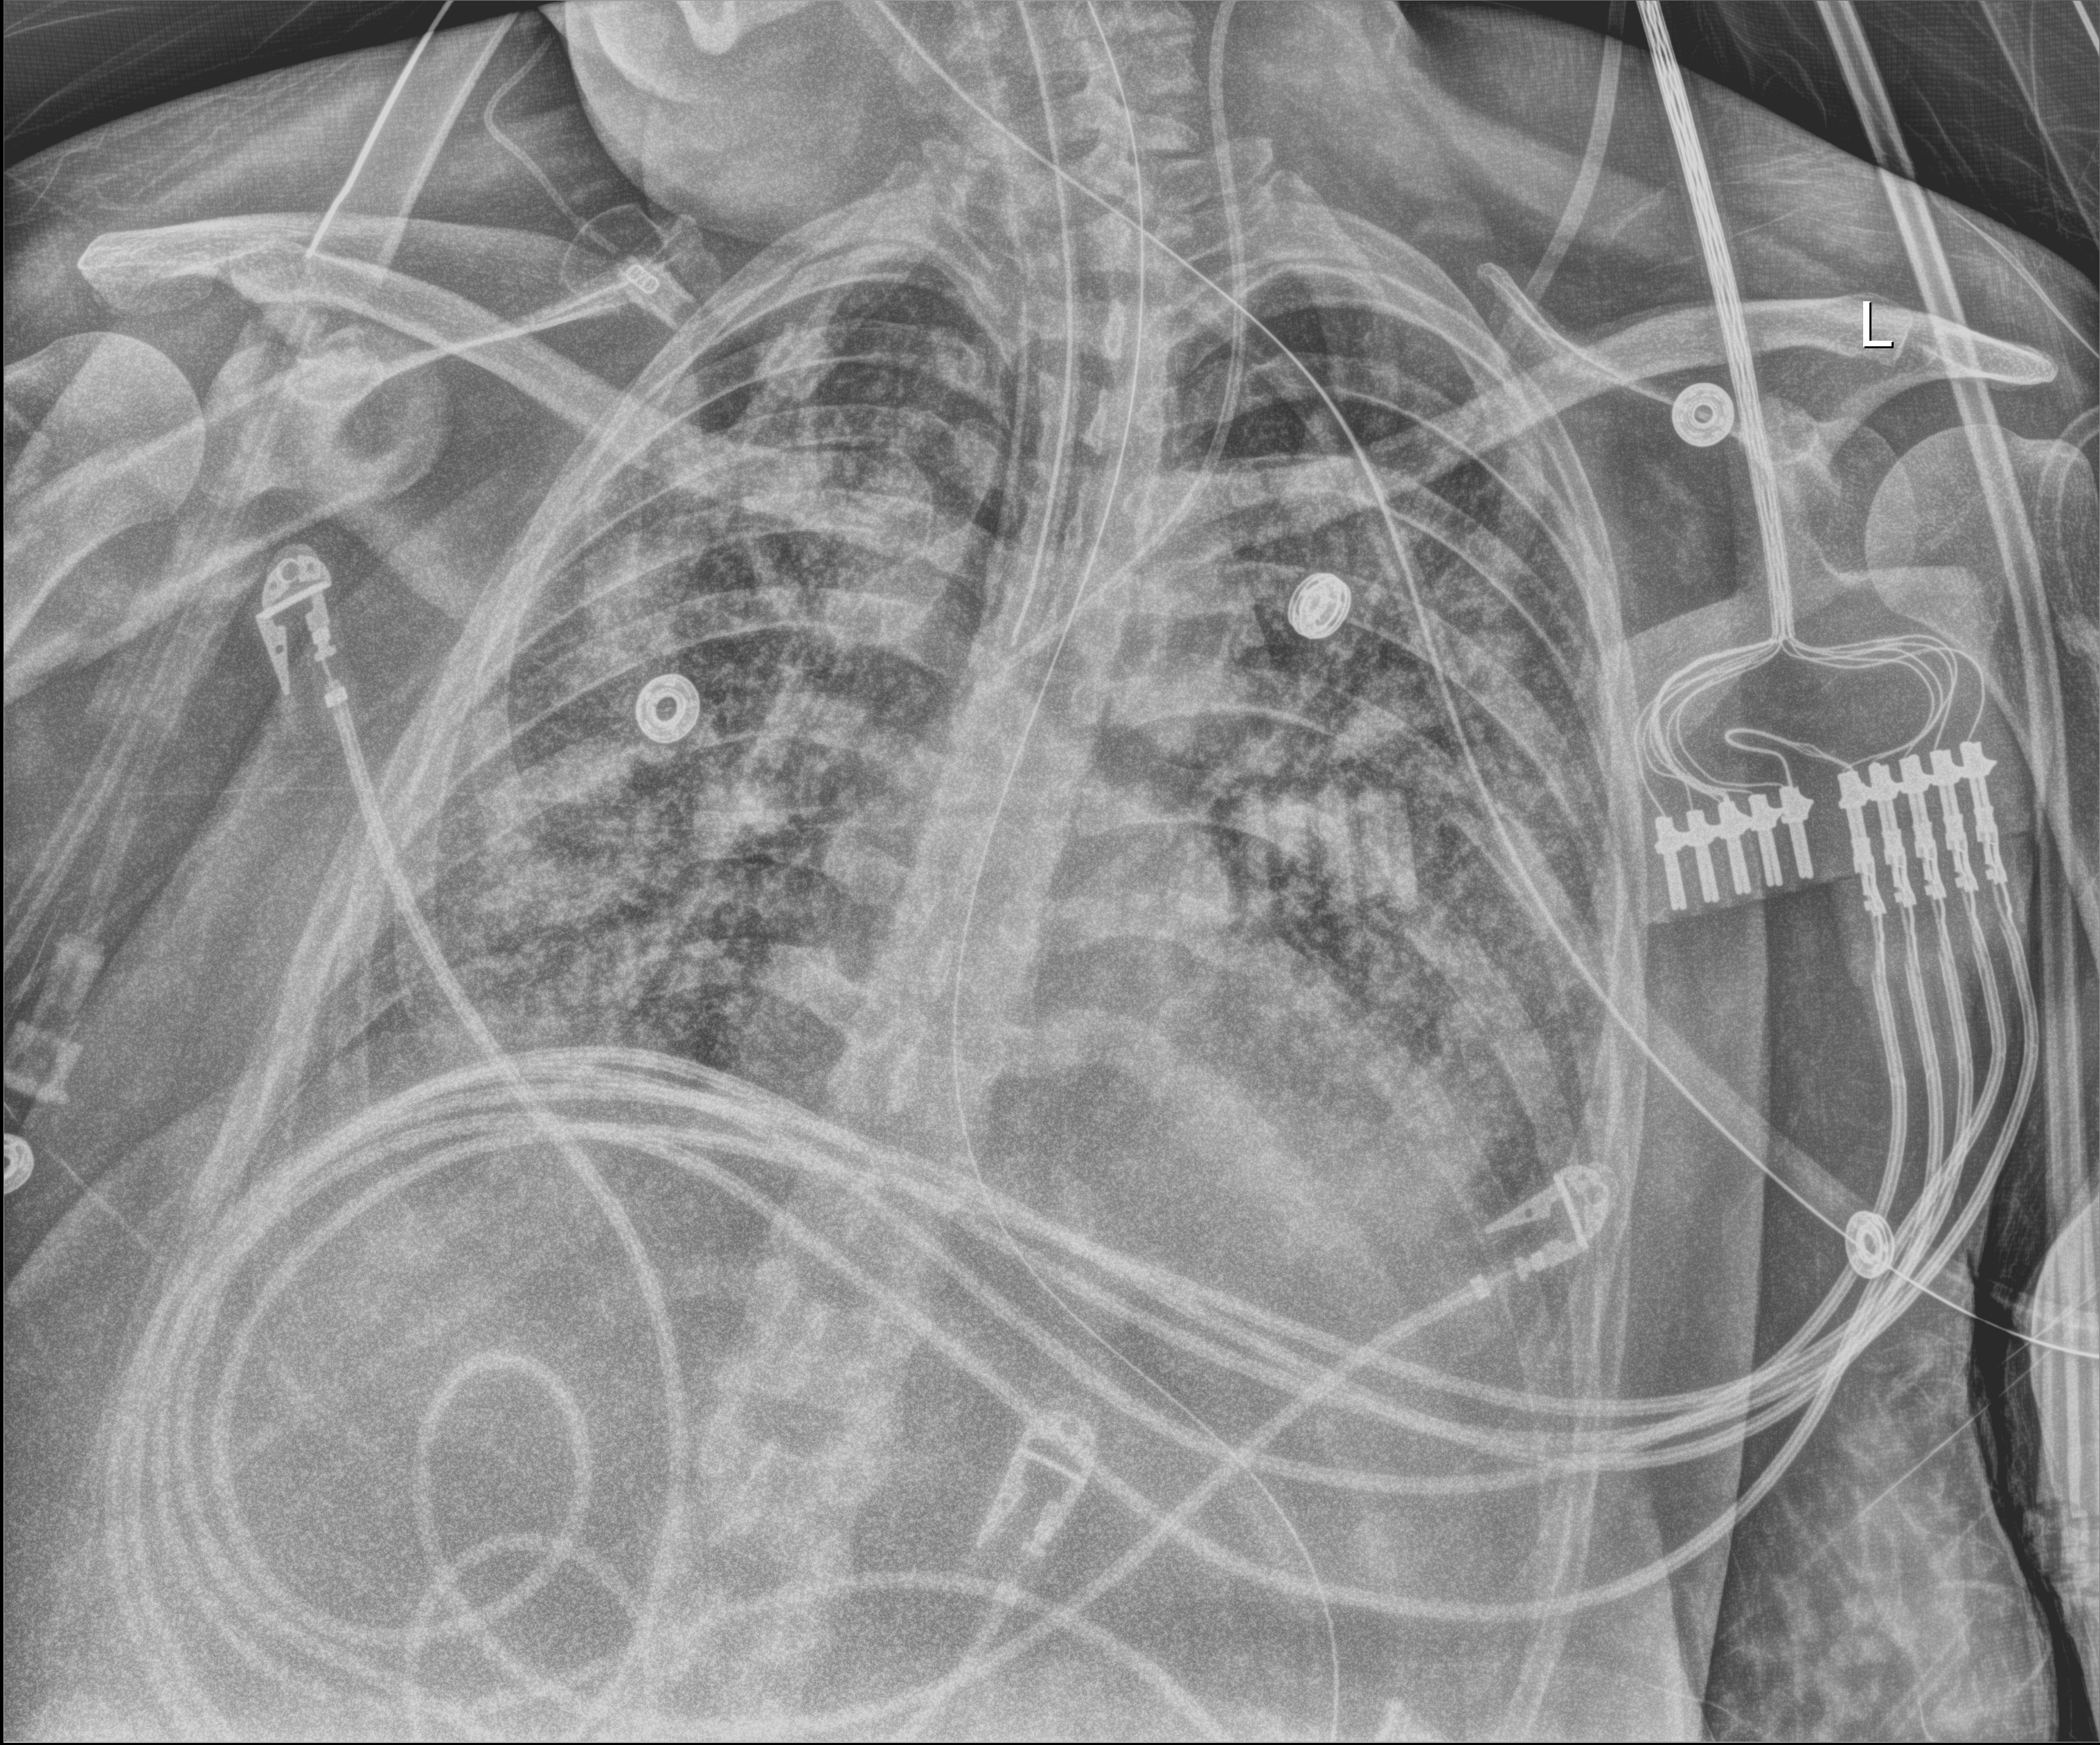
Portable chest radiograph, anteroposterior (AP) projection. Female patient hospitalised with COVID-19, age 18–59 years.
From the hospital-stay record, not from the radiograph (when in the stay this image was taken is not recorded):
- mechanically ventilated during this hospital stay: yes
- length of hospital stay: 33 days